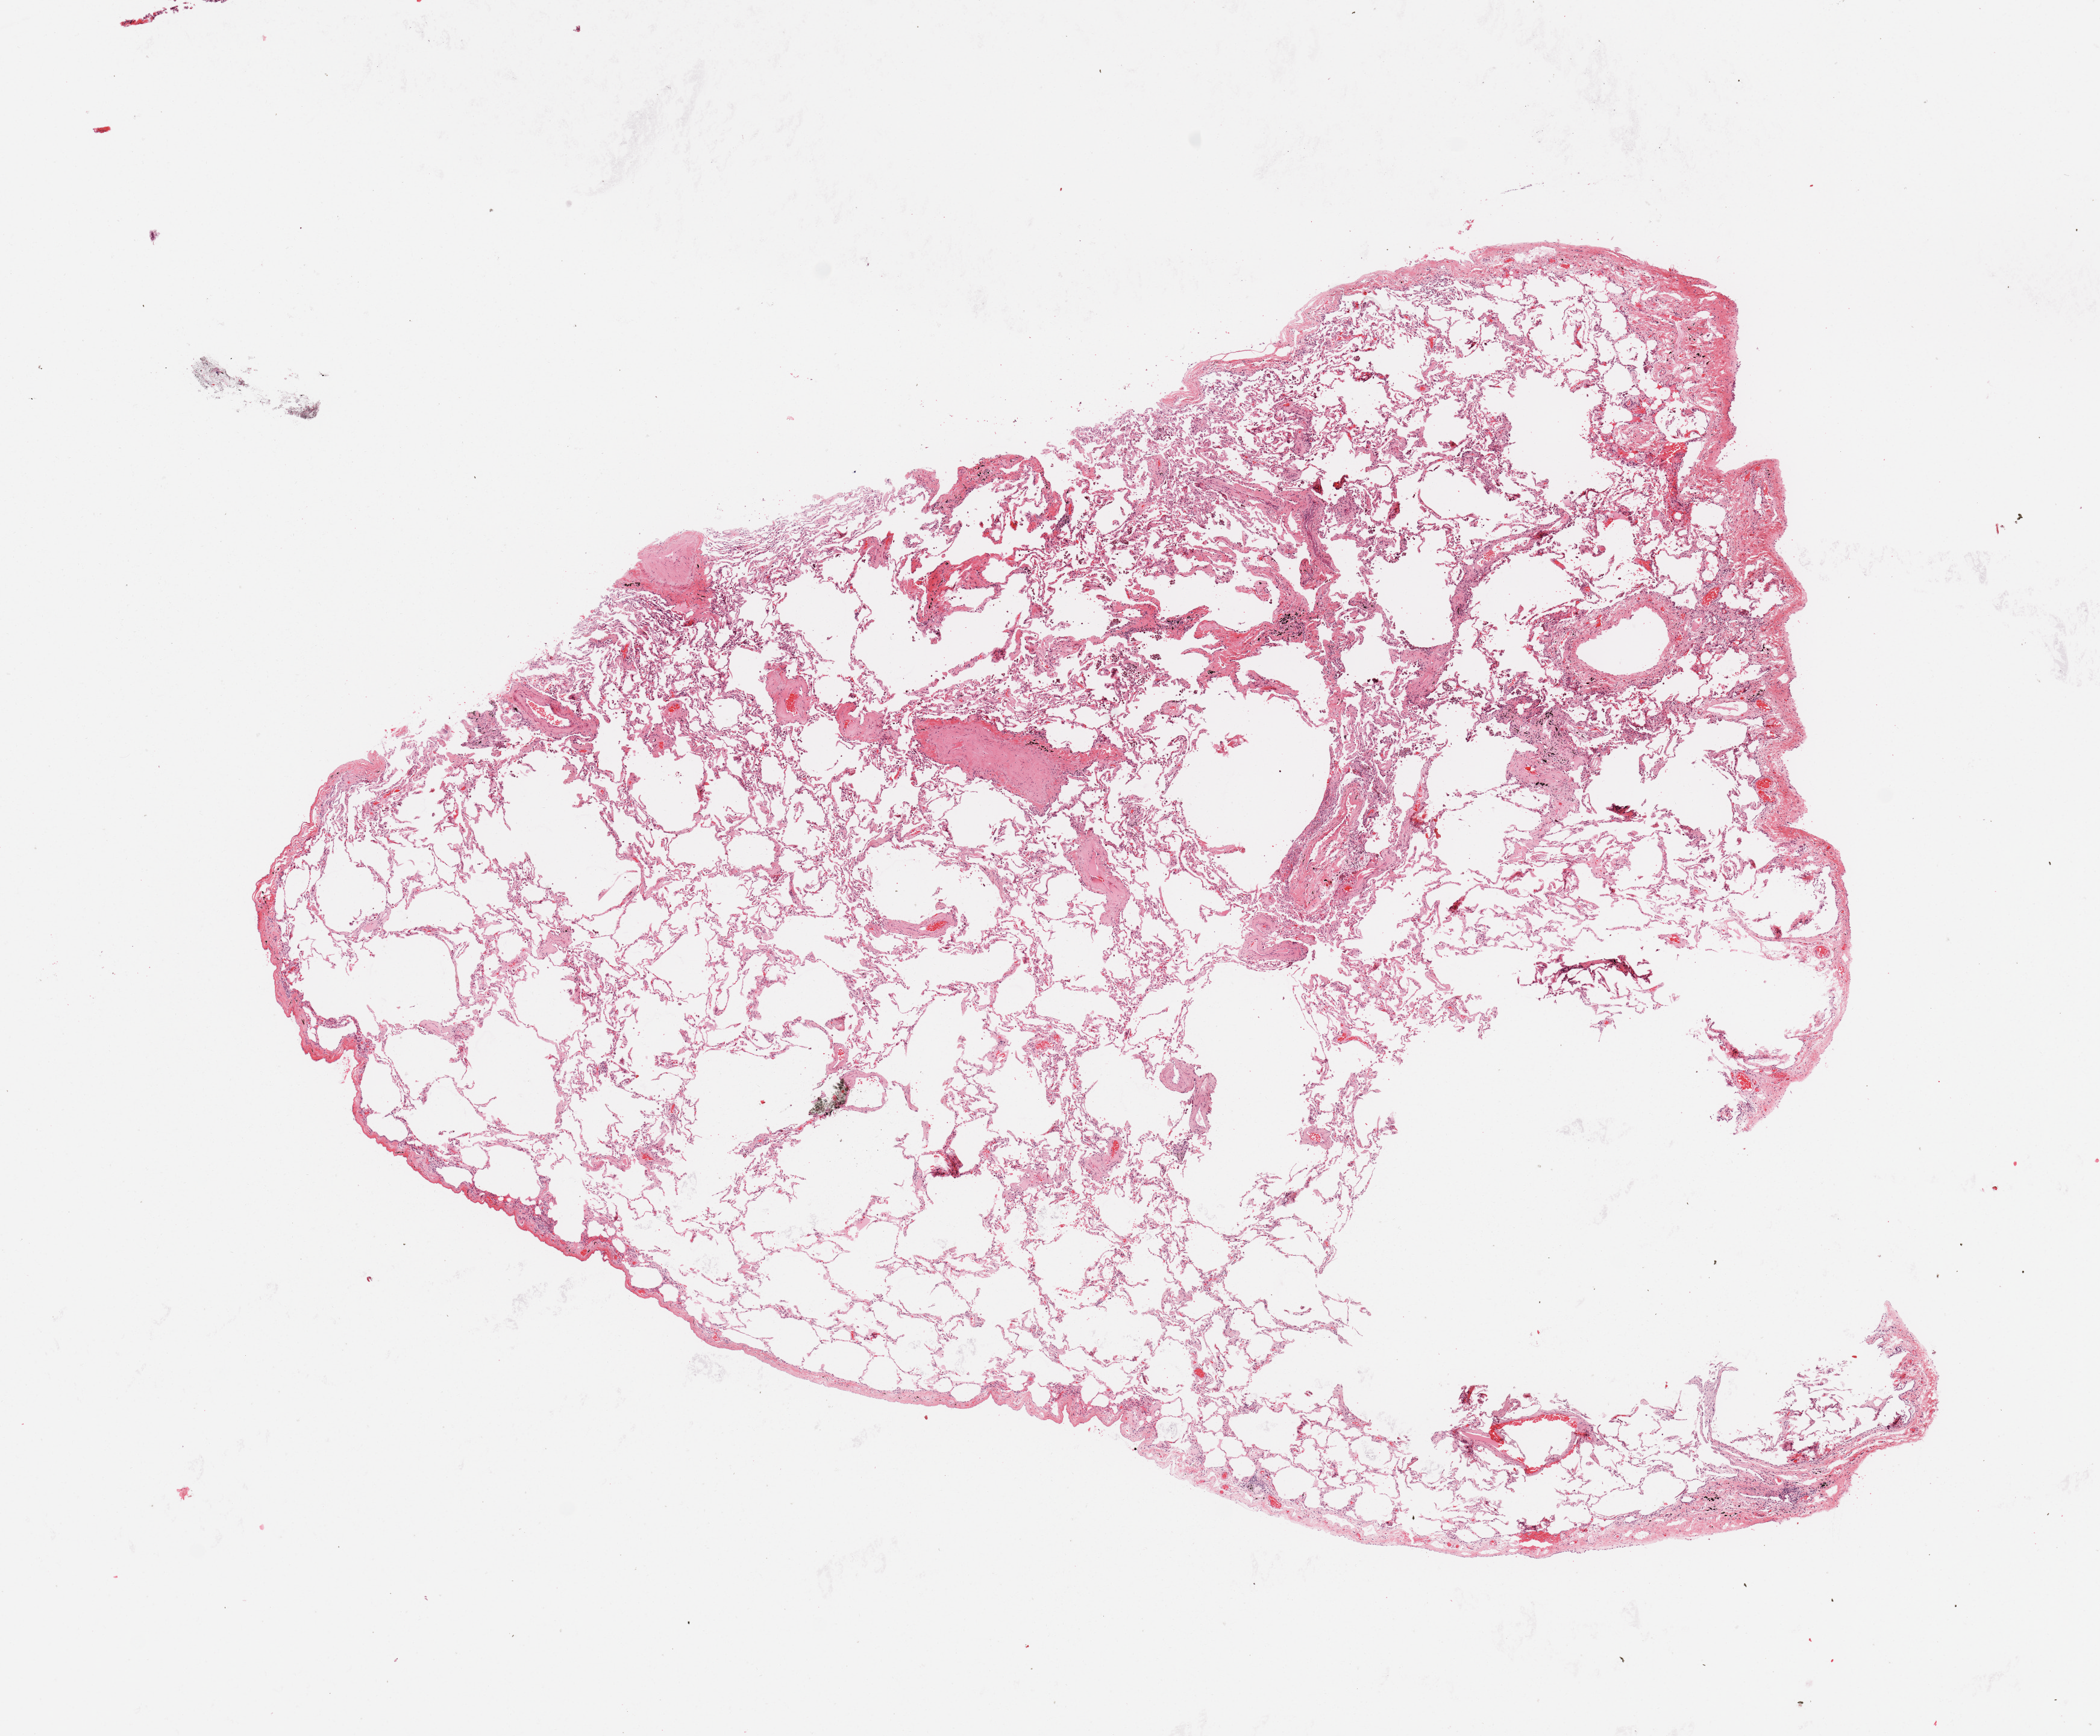
Digitized H&E tissue section (whole slide) — whole scanned area (about 13.8 x 11.4 mm) shown as a low-resolution overview; normal (non-tumour) tissue sample, sampled site: lung. Patient: male, age 66 years.
This section: normal (non-tumour) tissue from the same patient. Patient diagnosis: Adenocarcinoma, NOS.